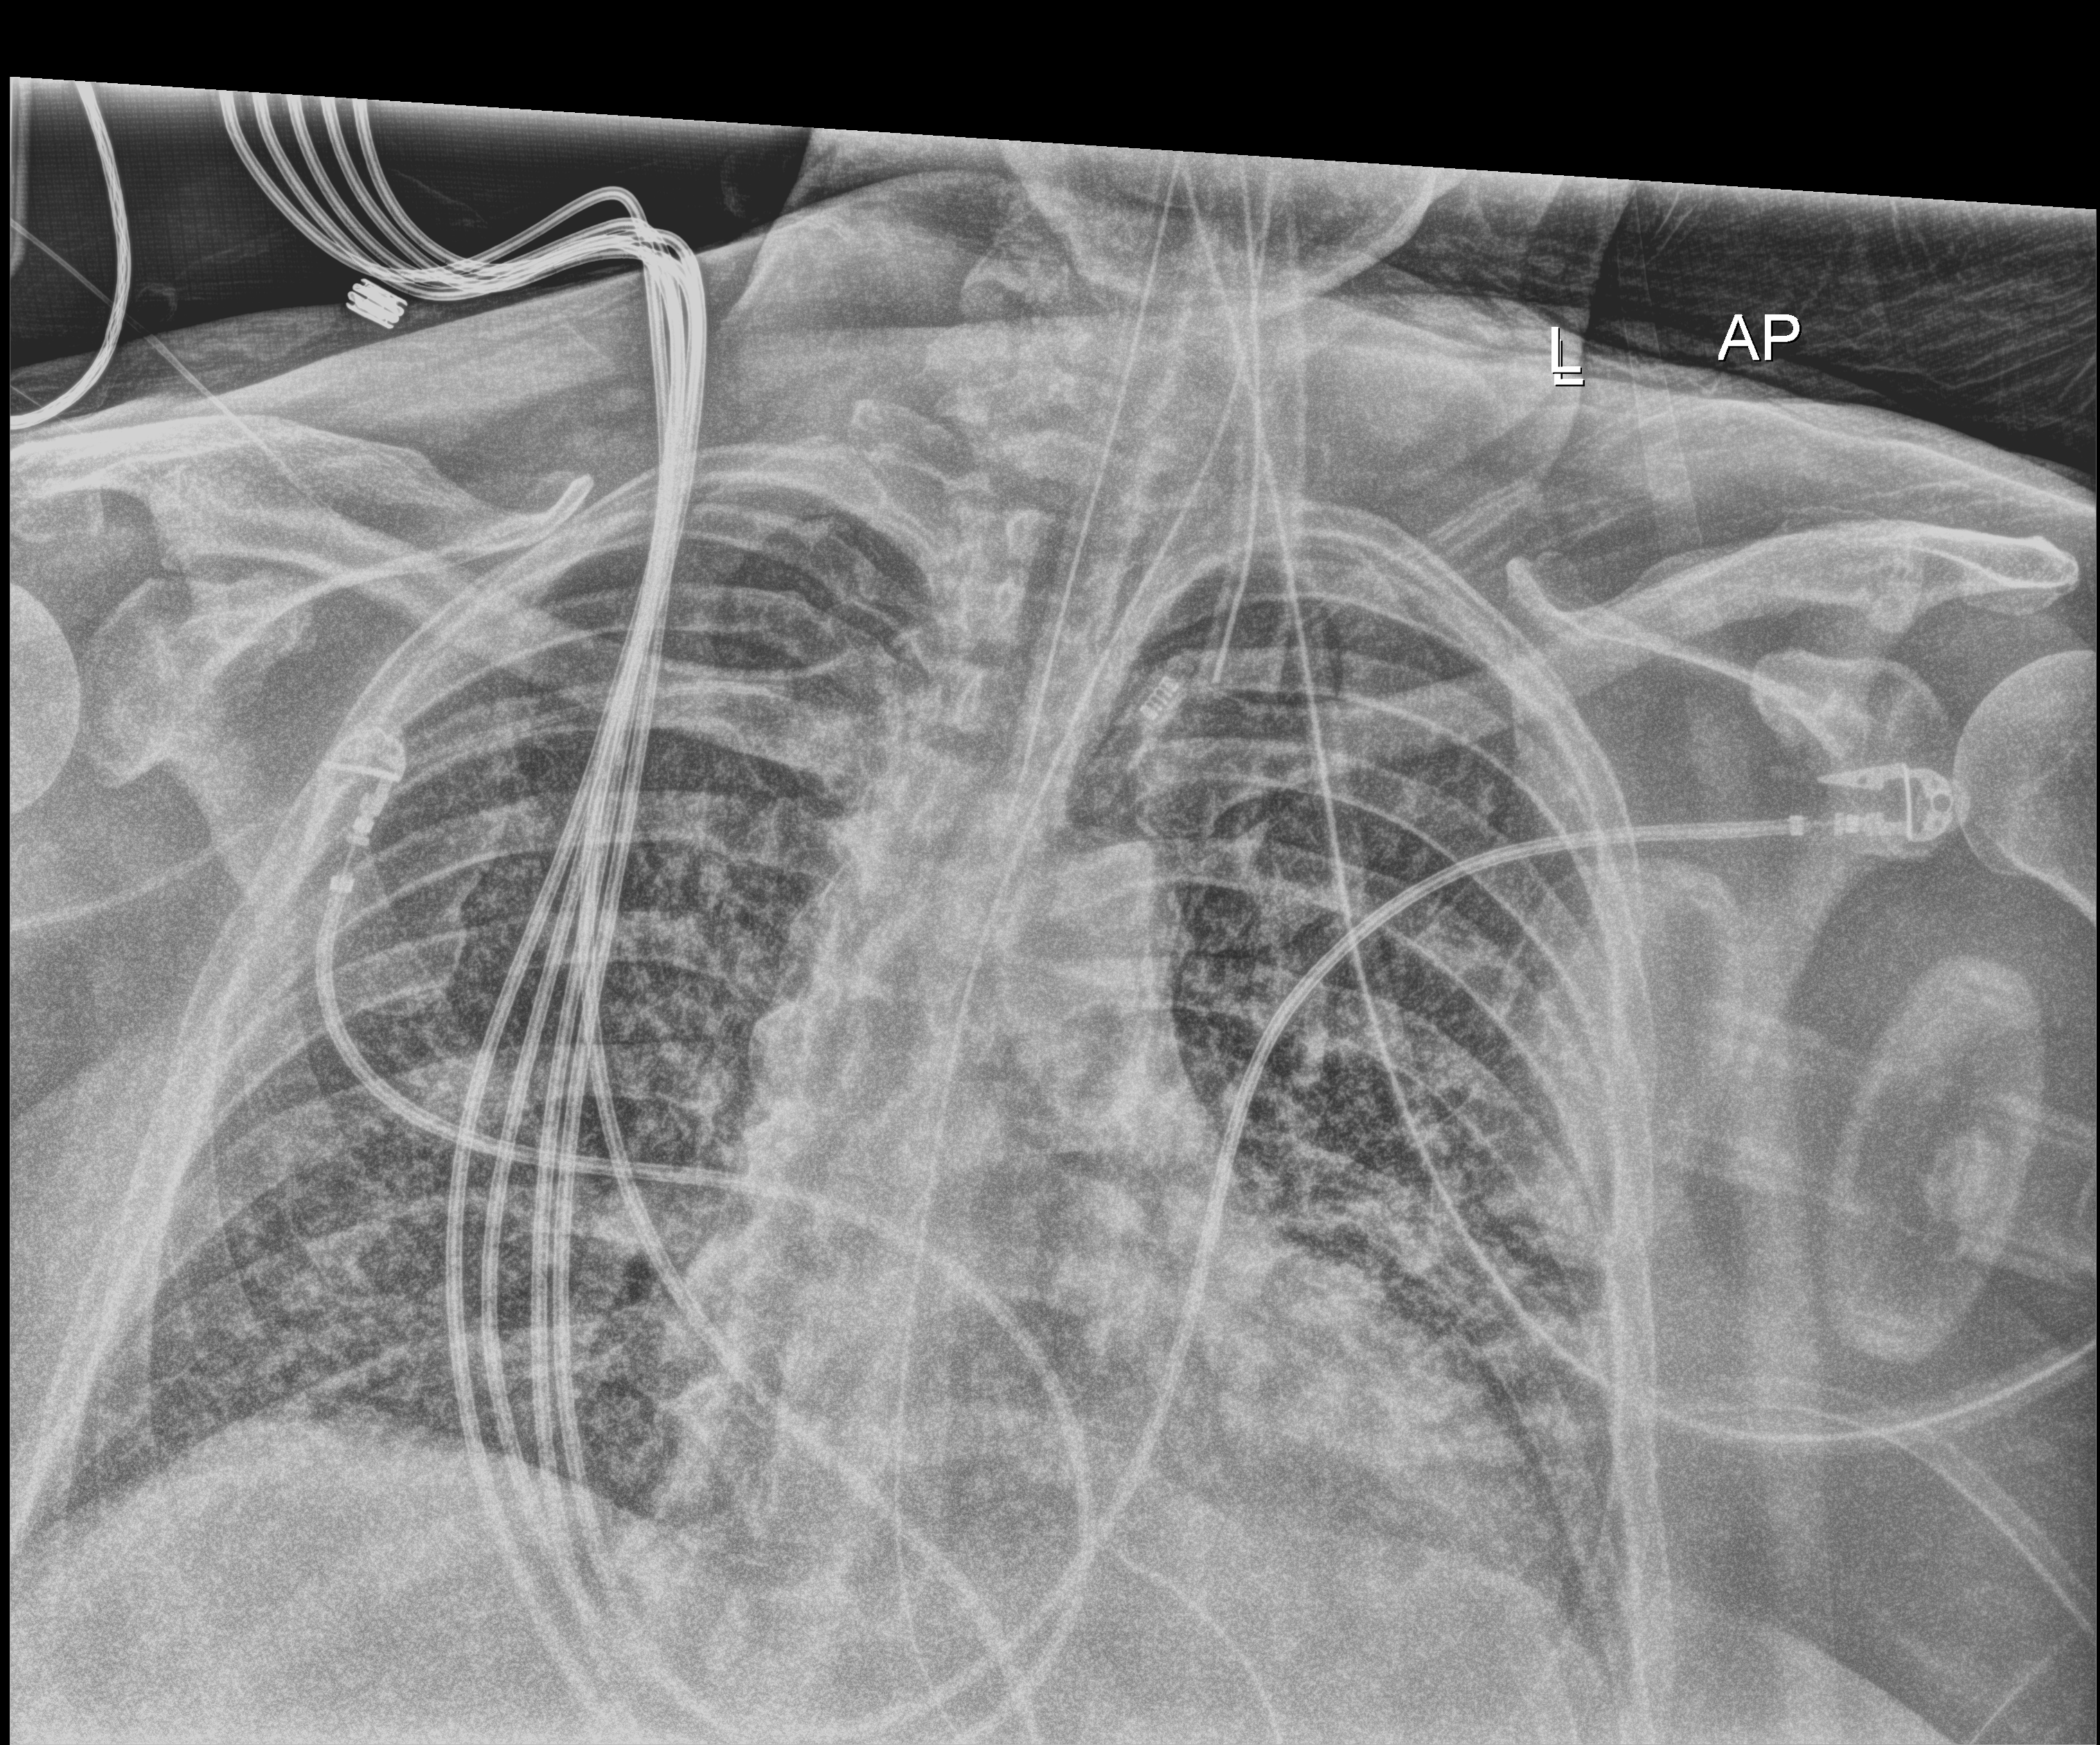
Chest X-ray; anteroposterior (AP) projection. Patient hospitalised with COVID-19, aged 18–59 years.
From the hospital-stay record, not from the radiograph (when in the stay this image was taken is not recorded): admitted to intensive care during this hospital stay: yes; mechanically ventilated during this hospital stay: yes; length of hospital stay: 28 days.